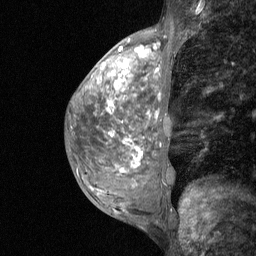
Breast MRI (dynamic contrast-enhanced), one sagittal slice; dynamic contrast-enhanced study with each time point stored as its own series, time point 2 of 3 at this slice position (early post-contrast, ordered by acquisition time); 1.5 T; TE 4.8 ms, TR 27 ms; 2 mm slice thickness; 256 × 256 image matrix, field of view 200 × 200 mm. Female patient, age 36 years. From the clinical record (not read from this slice): setting: breast cancer imaged before/during neoadjuvant chemotherapy; receptor status: HR-positive, HER2-negative.
Structures marked on this image (semi-automatically segmented with operator editing):
- analysis volume of interest (the breast-tissue region the enhancement analysis was run in; not a lesion): bounding box [x1, y1, x2, y2] px = [73, 57, 174, 210]
- tumour enhancement mask (voxels above the 90 % enhancement threshold inside the analysis volume of interest): [112, 59, 128, 83]